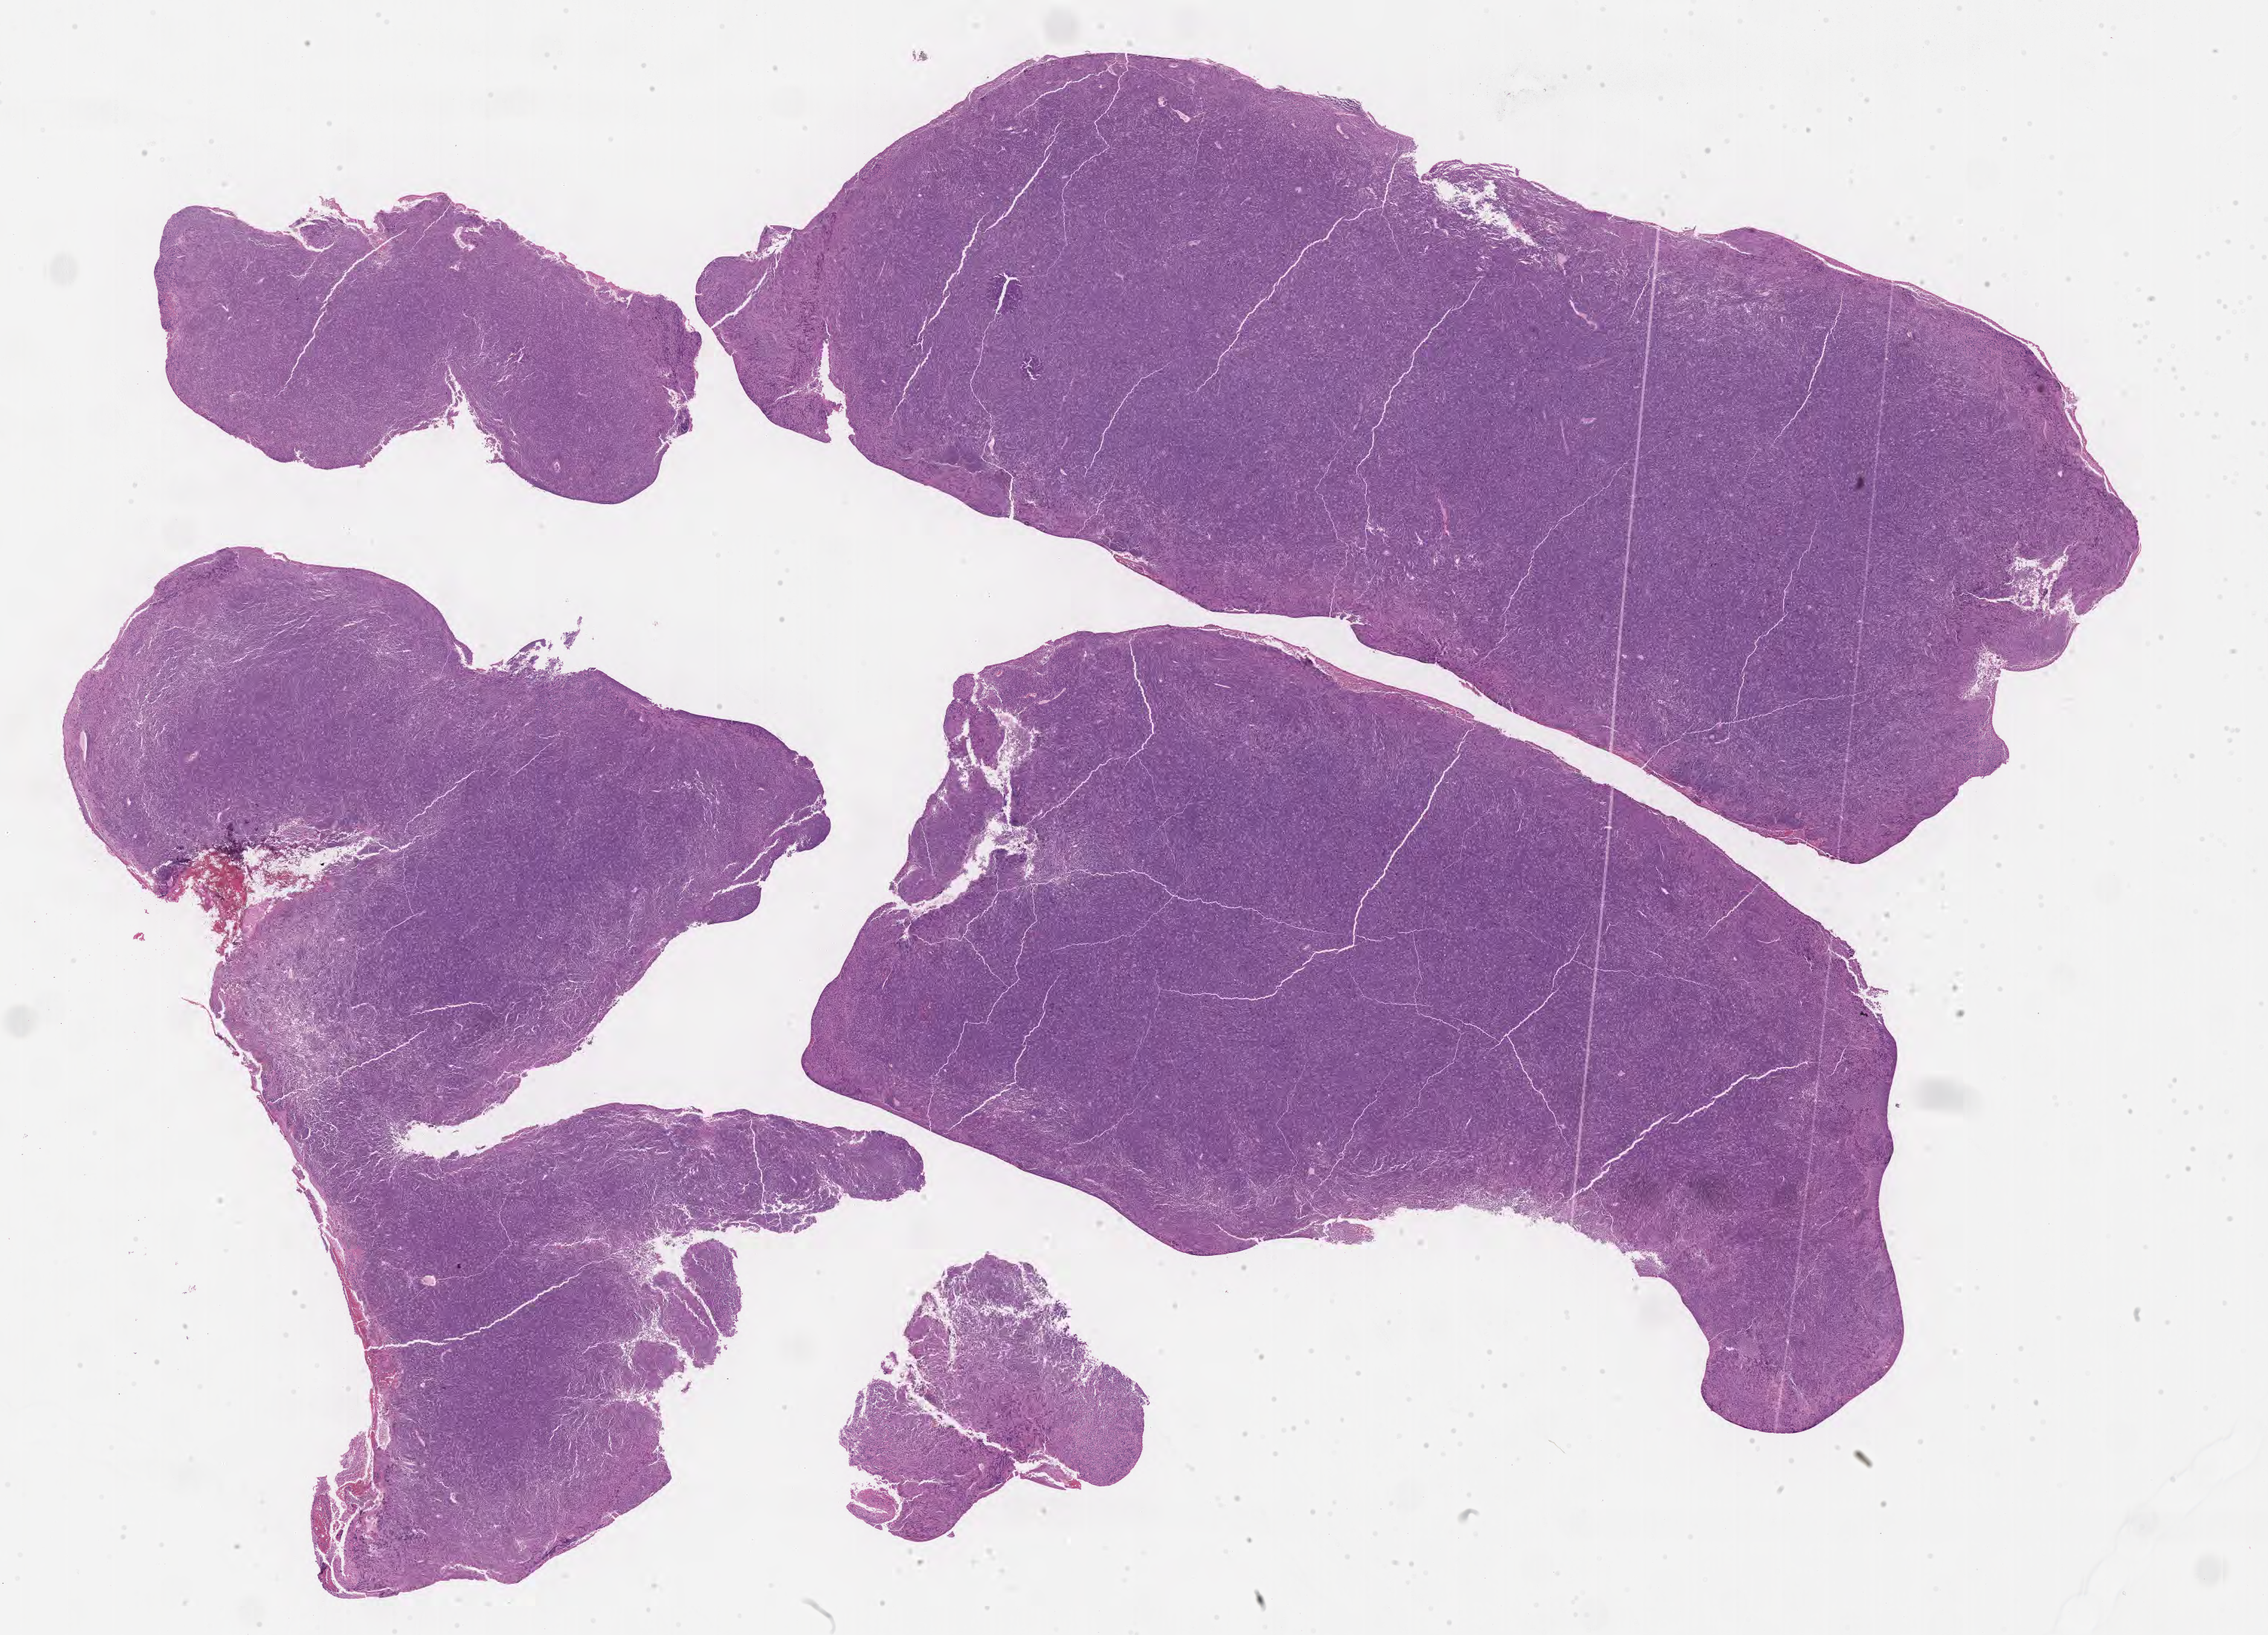
Digitized hematoxylin and eosin (H&E)-stained section, shown as a low-resolution overview of the whole scanned area (about 24.7 x 17.8 mm); tumor tissue; site: peritoneum. Patient: female, age at initial diagnosis 7 years.
Histologic diagnosis: Burkitt lymphoma, NOS.